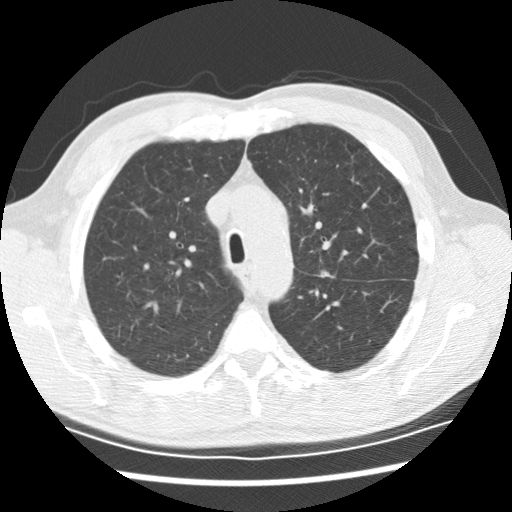
Low-dose screening chest CT, one axial slice; position 149 of 208 along the scan axis; reconstruction kernel STANDARD; 120 kVp; lung window (W 1500 / L -600 HU); 2.5 mm slice thickness; 512 × 512 image matrix.
Structures marked on this image (expert manual segmentation):
- lesion 1 (tumor, upper lobe of left lung): bounding box (x1, y1, x2, y2) in pixels: (321, 270, 332, 276)